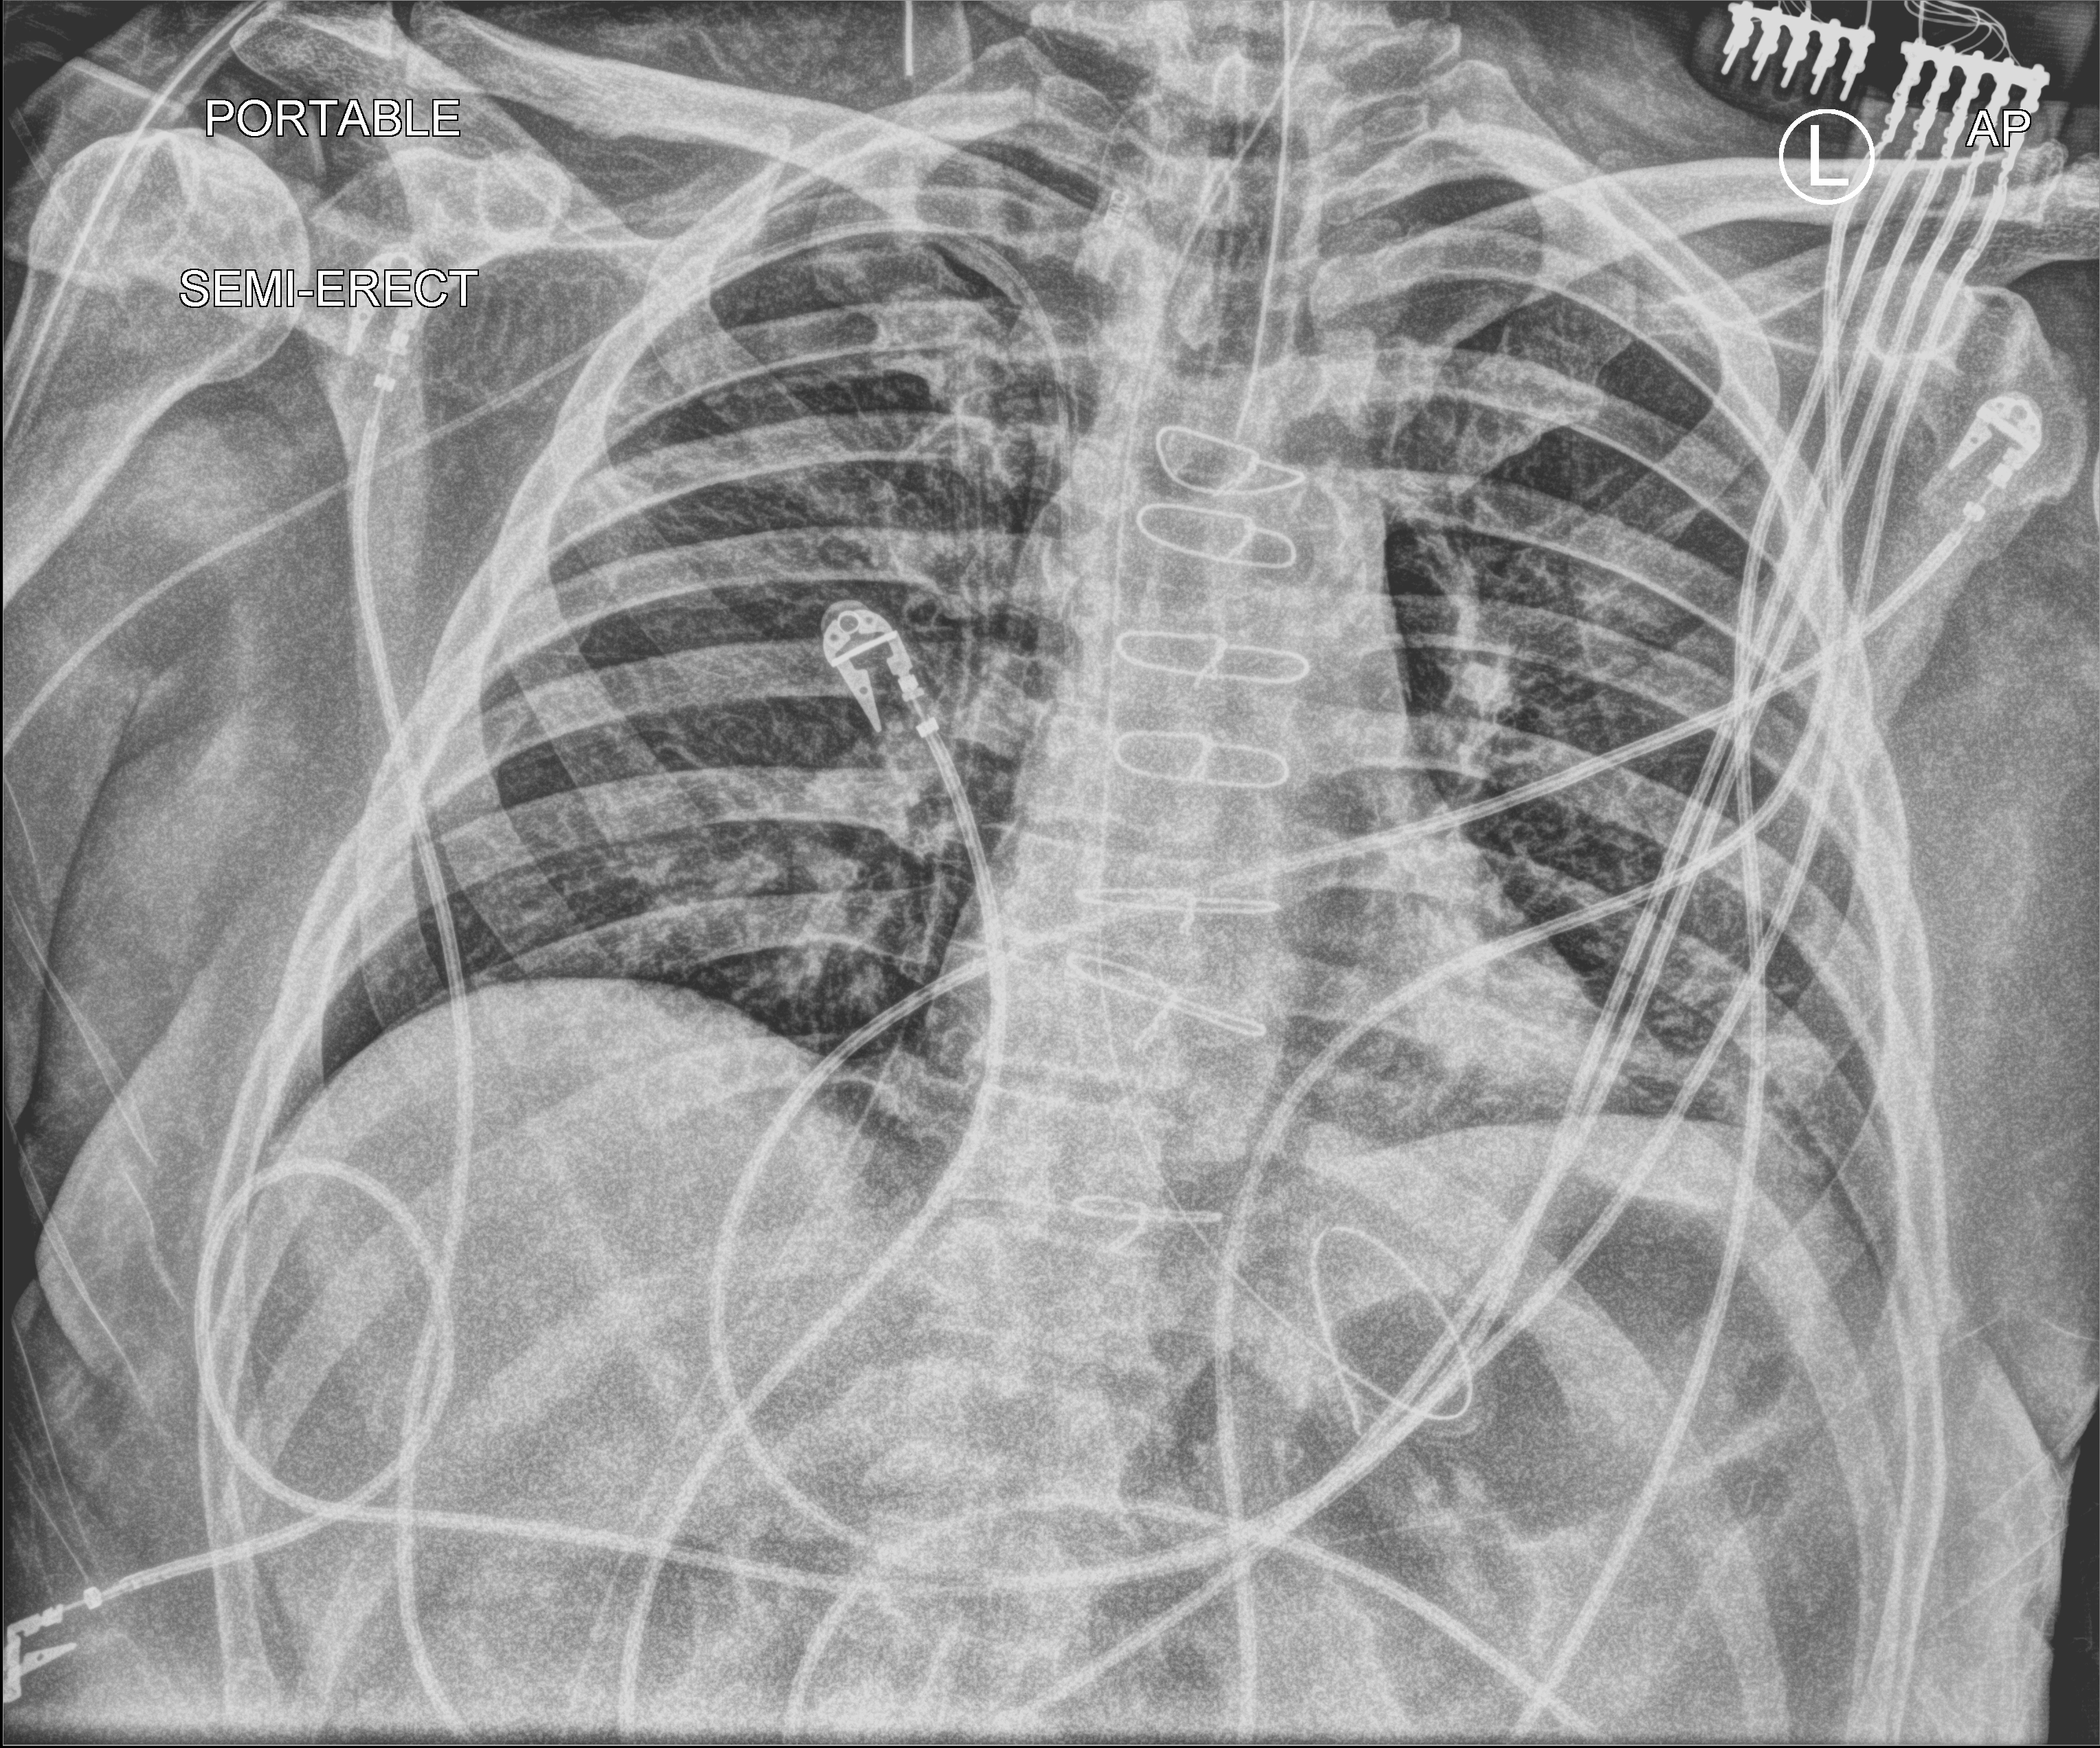
Chest X-ray (portable), anteroposterior (AP) projection. Patient hospitalised with COVID-19; male, aged 60–74 years.
From the hospital-stay record, not from the radiograph (when in the stay this image was taken is not recorded): COPD (admission record): no; mechanically ventilated during this hospital stay: yes.